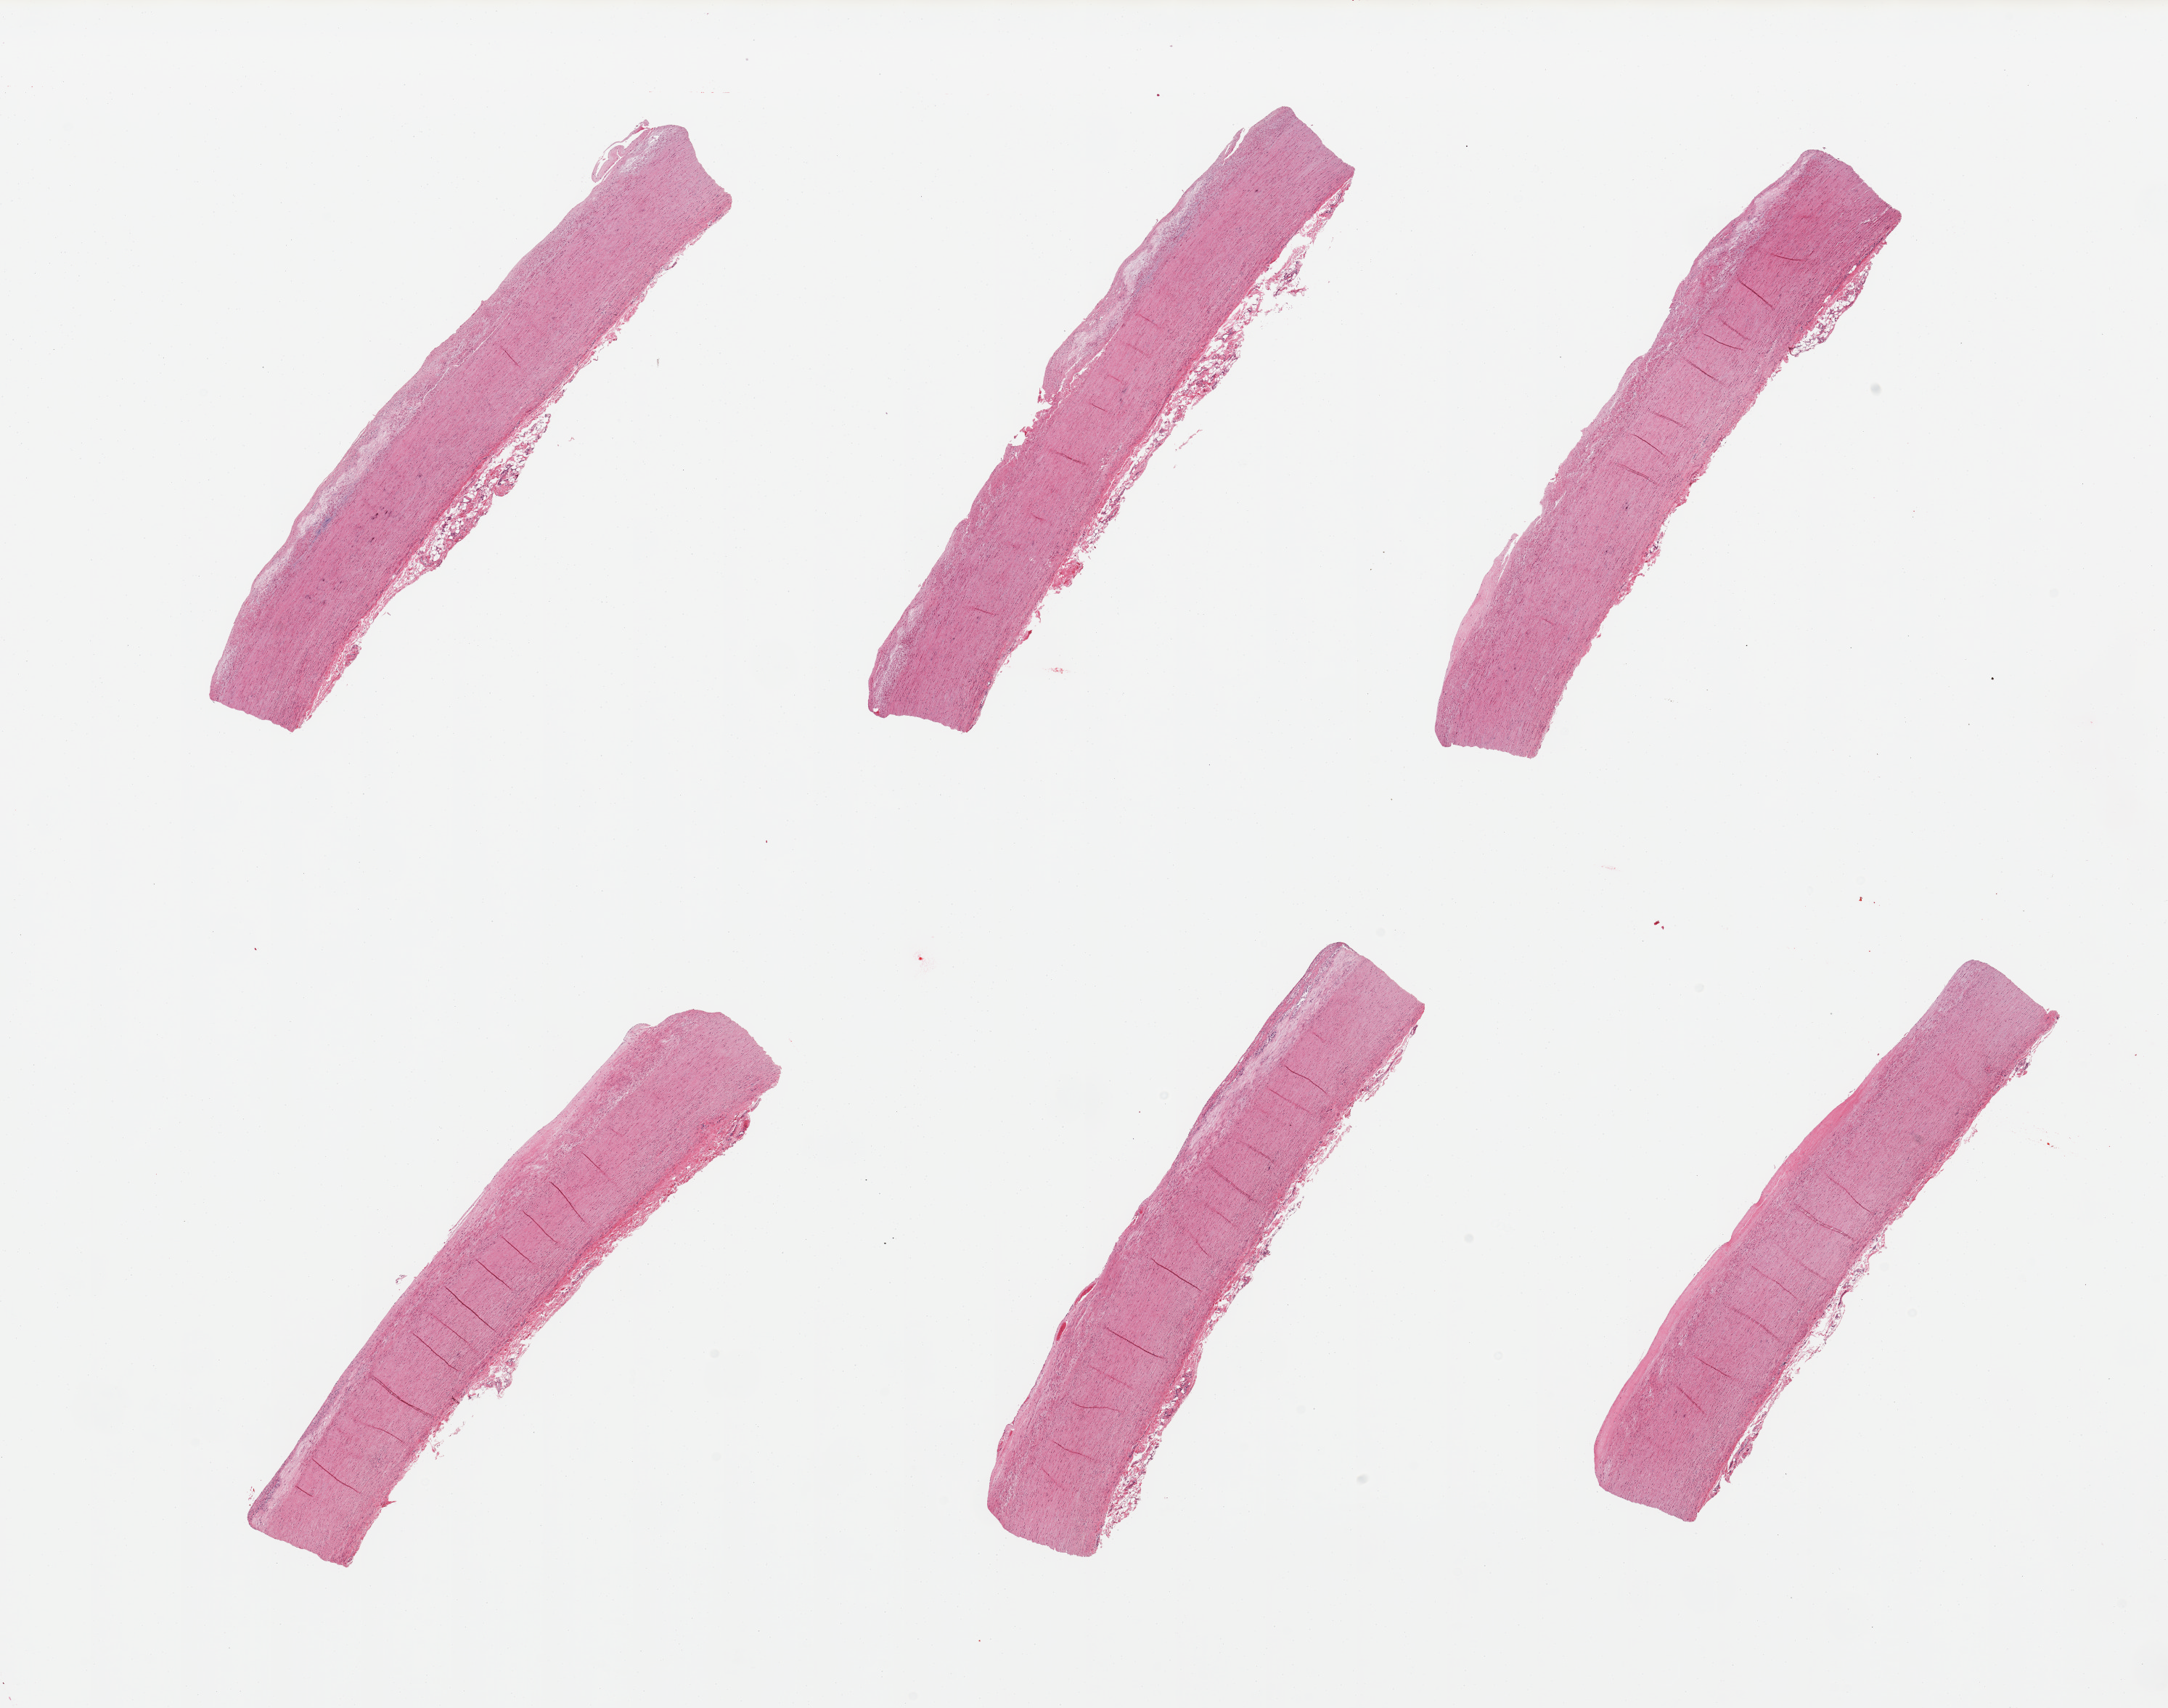
Digitized H&E-stained section — a low-resolution overview of the entire scanned area, about 23.6 x 18.6 mm (from a 20x scan), PAXgene-fixed paraffin-embedded (PFPE) section, sampled site (target tissue): aorta, donor tissue sample. Male donor.
- pathologist's review note for this sample: 6 pieces; well dissected; thin flat plaques